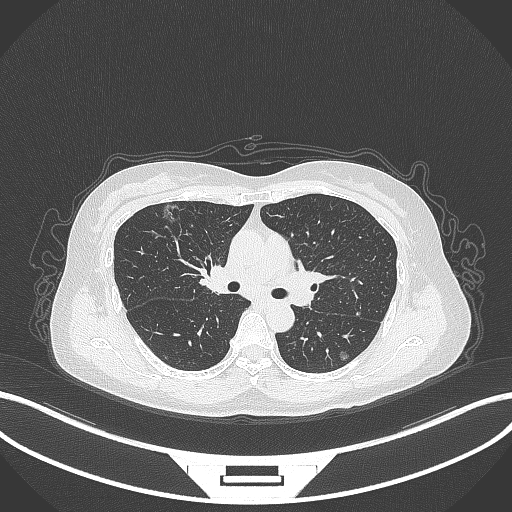
Chest CT, one axial slice. Position 201 of 315 along the scan axis. 120 kVp. Lung window (W 1500 / L -600 HU). 512 × 512 image matrix, field of view 400 × 400 mm. Female patient, age 61 years. From the clinical record (not read from this slice): clinical TNM (as recorded): T1b N0 M0.
Annotated regions visible in this slice (bounding box drawn by a radiologist):
- lung tumour (recorded histology: adenocarcinoma): bounding box <158,199,187,226> (left, top, right, bottom; pixels)